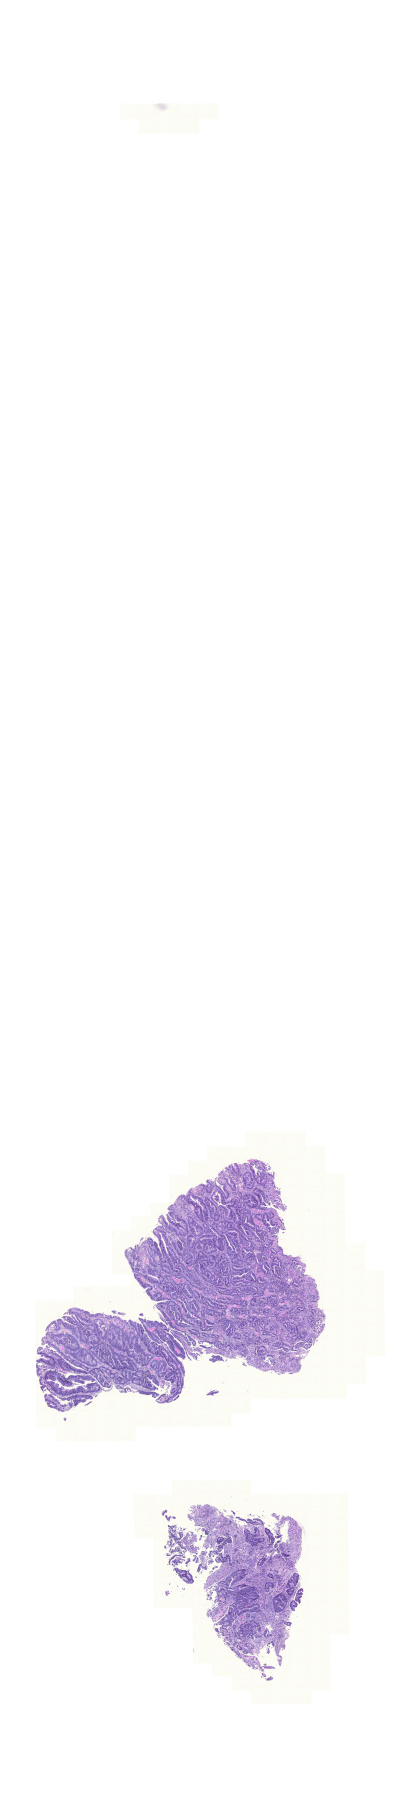
Whole-slide histology image, Hematoxylin and eosin (H&E) stained, whole scanned area (about 6.1 x 26.7 mm, slide scanned at 20x) shown as a low-resolution overview. FFPE section. Colon, primary tumour sample. Patient: male, age at initial diagnosis 66 years.
AJCC pathologic stage: IIIC (6th edition). Lymph nodes positive (case pathology): 7 of 25 examined. Diagnosis: Adenocarcinoma, NOS (sigmoid colon).